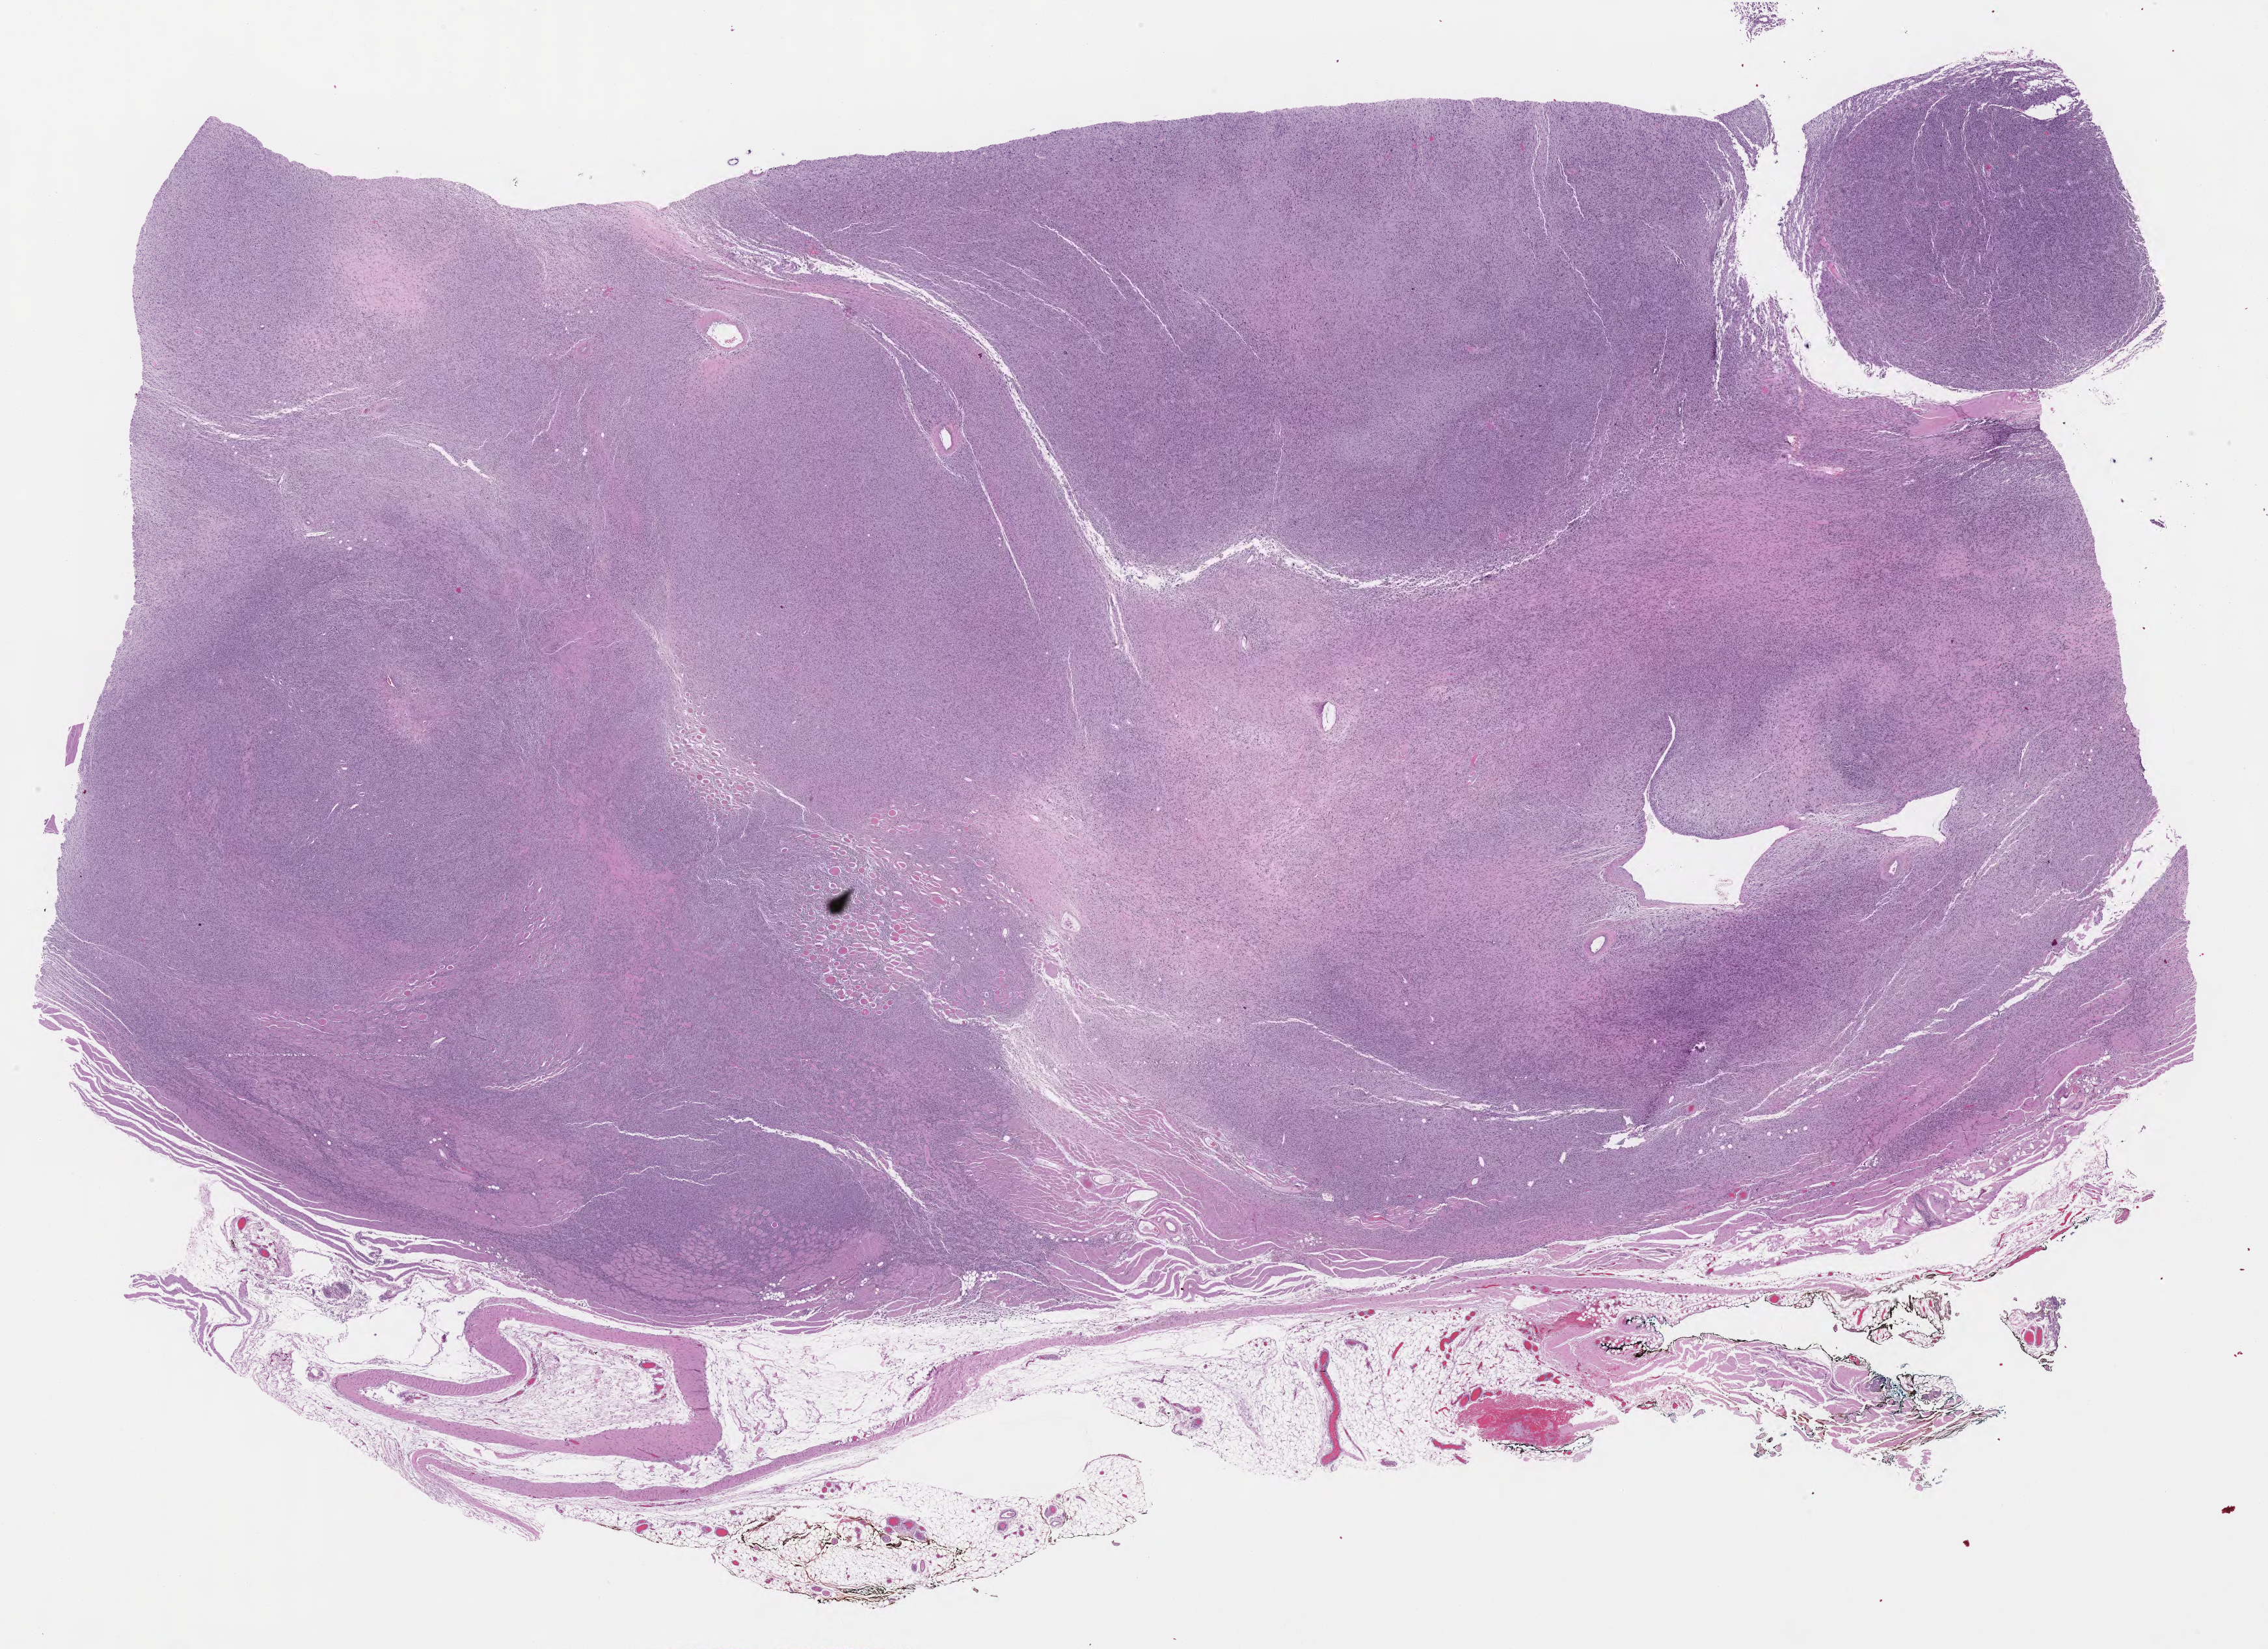
H&E whole-slide image — shown as a low-resolution overview of the whole scanned area (about 28.0 x 20.4 mm, acquisition: 40x scan); FFPE section; sample: primary tumour, connective, subcutaneous and other soft tissues. Patient: female, age at initial diagnosis 78 years.
Diagnosis: Undifferentiated sarcoma (connective, subcutaneous and other soft tissues of lower limb and hip).